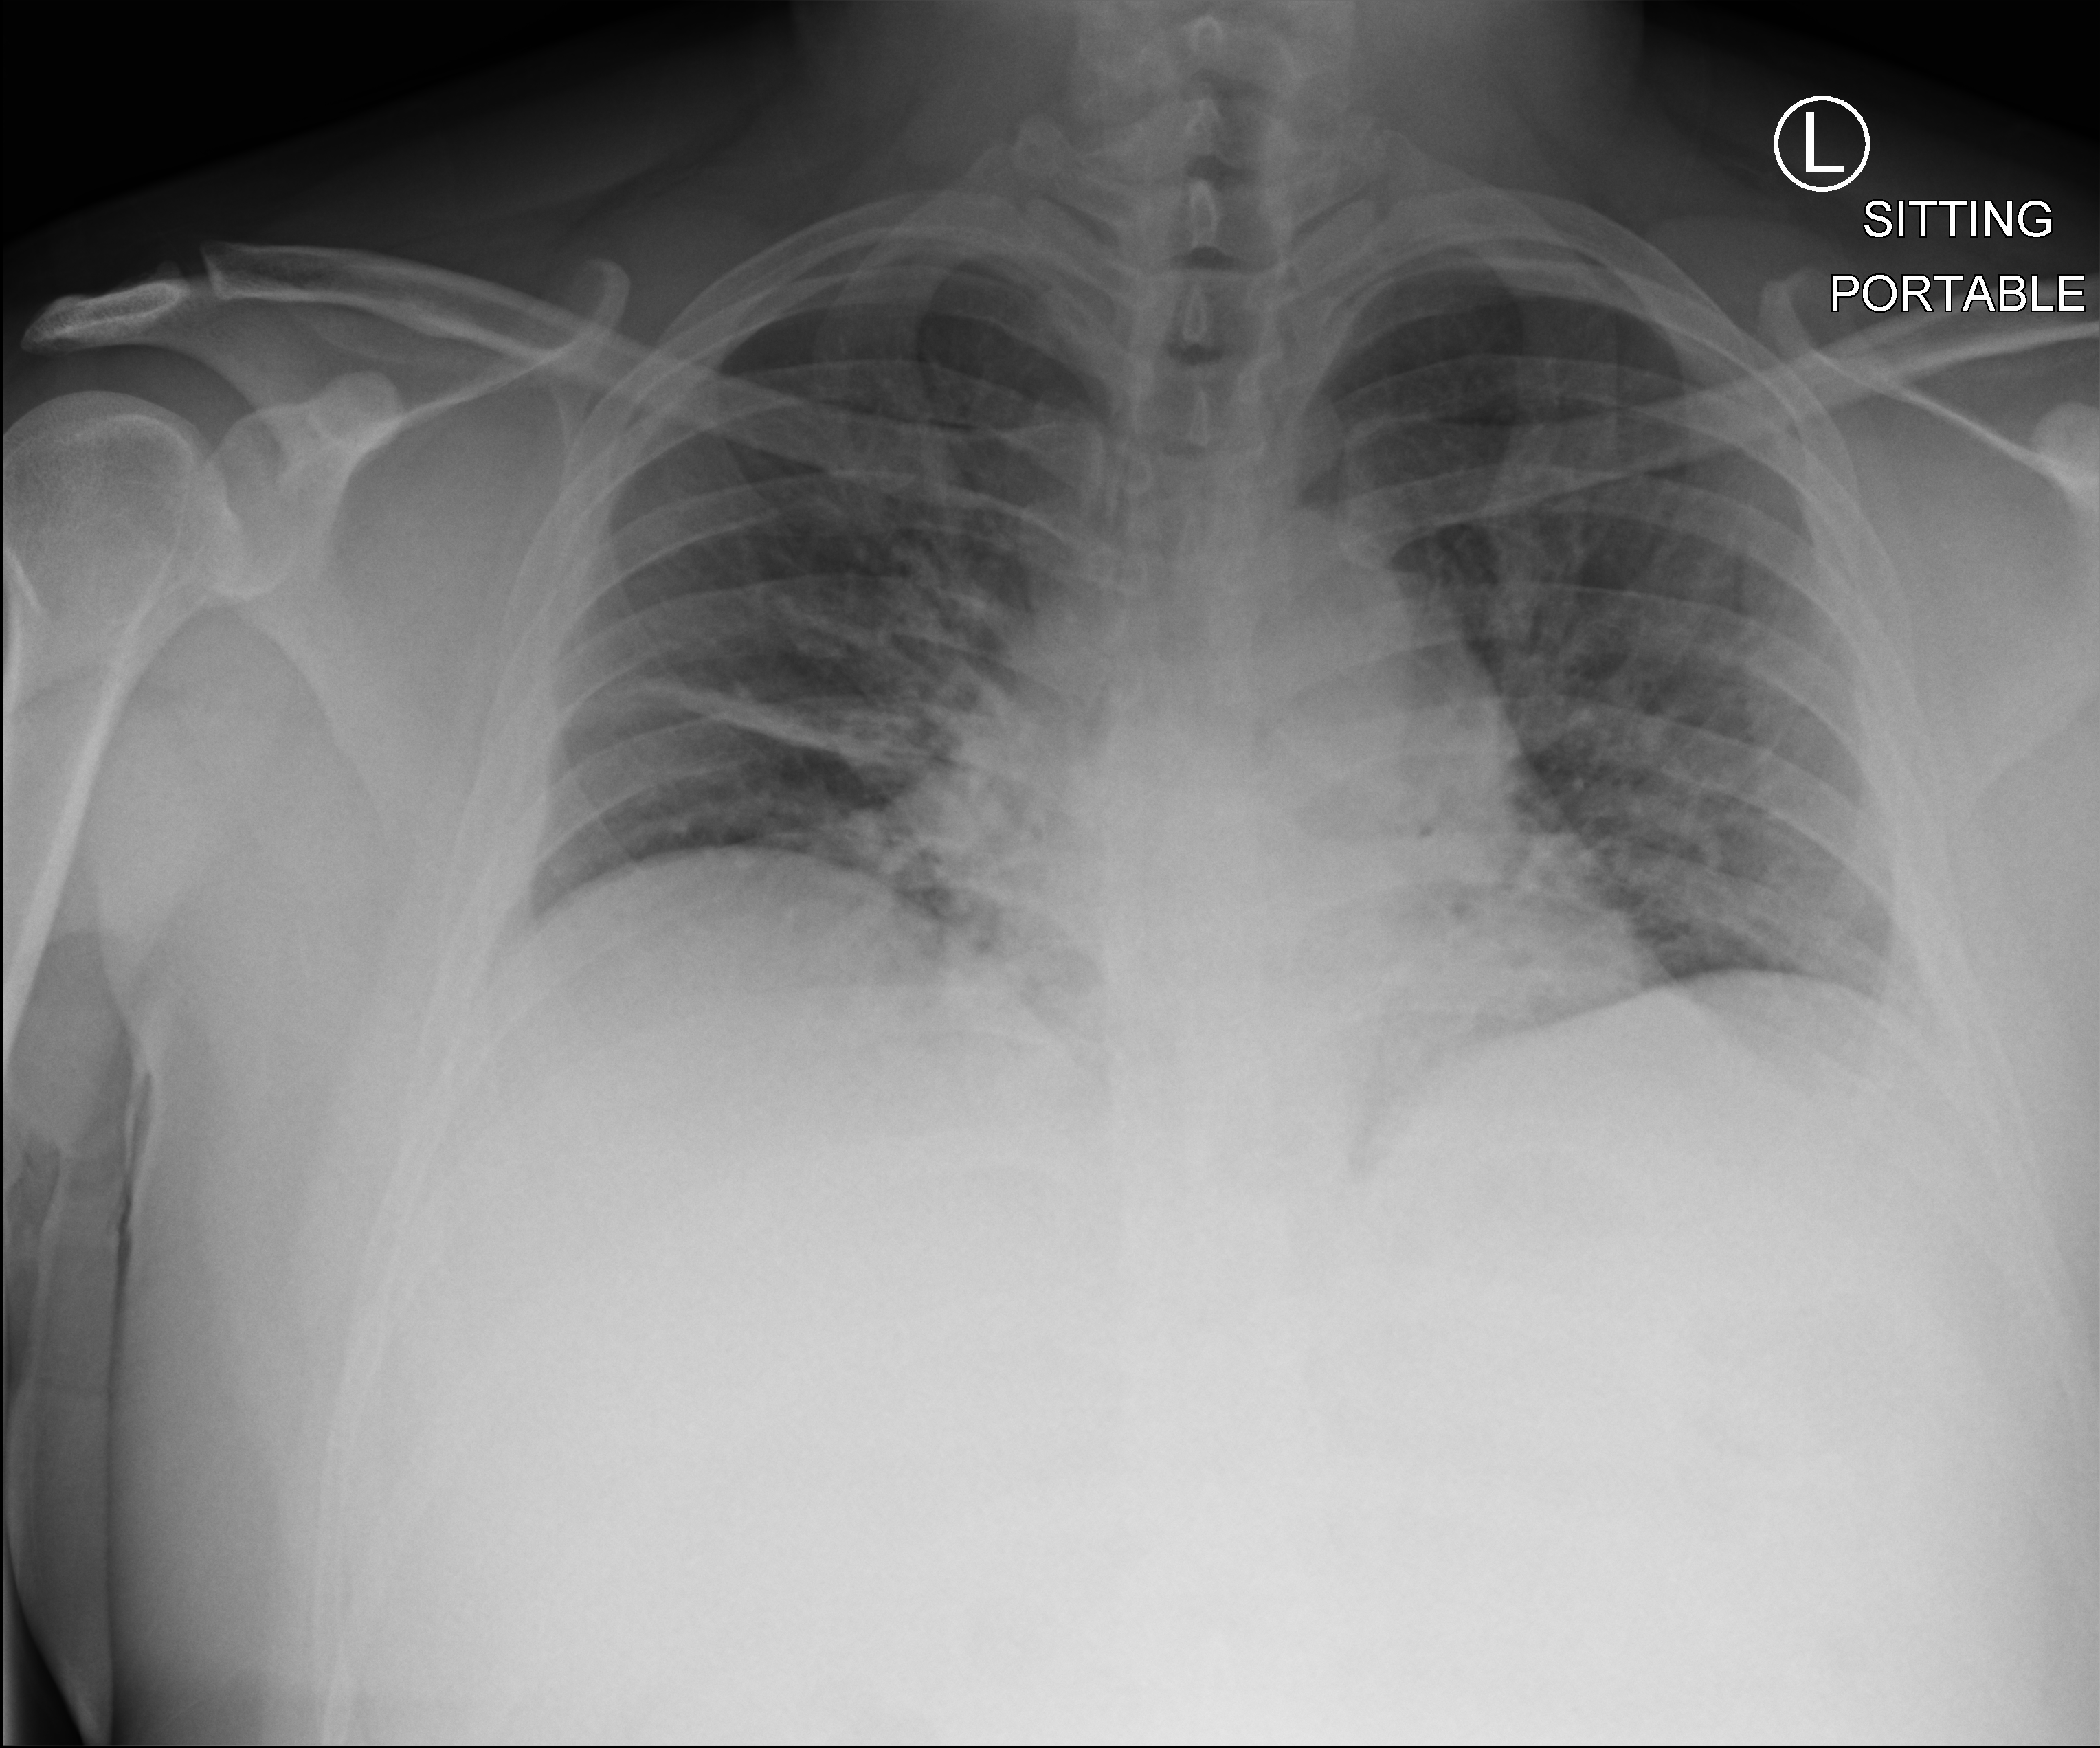
Bedside chest radiograph (computed radiography). Male patient hospitalised with COVID-19, age 18–59 years.
Hospital-stay facts (about this admission, not read from this image; timing relative to this image not recorded): admitted to intensive care during this hospital stay: no; mechanically ventilated during this hospital stay: no.